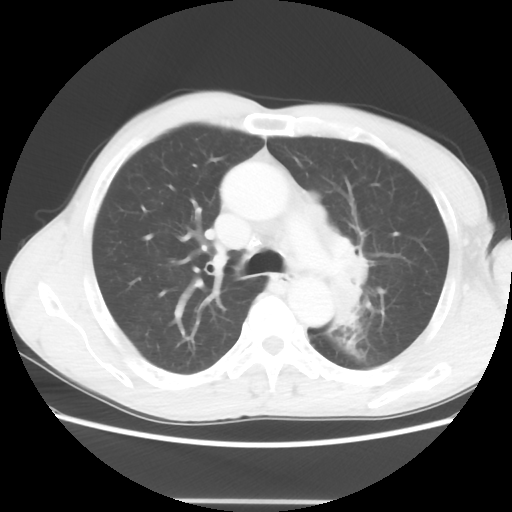
Chest CT, one axial slice; reconstruction kernel STANDARD; lung window (W 1500 / L -600 HU); 5 mm slice thickness; 512 × 512 image matrix, field of view 360 × 360 mm. Male patient, age 61 years. From the clinical record (not read from this slice): clinical TNM (as recorded): T3 N1 M1.
Structures marked on this image (bounding box drawn by a radiologist):
- lung tumour (recorded histology: adenocarcinoma): box from (x=308, y=200) to (x=368, y=327) px